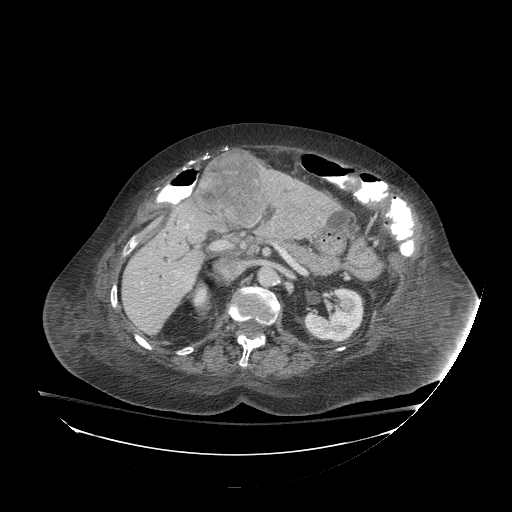
Contrast-enhanced abdominal CT (liver protocol), one axial slice; position 40 of 81 along the scan axis; 140 kVp; soft-tissue window (W 400 / L 40 HU); 2.5 mm slice thickness; 512 × 512 image matrix. From the clinical record (not read from this slice): diagnosis: hepatocellular carcinoma (patient treated with transarterial chemoembolisation; whether this scan precedes or follows treatment is not stated here); TNM stage (as recorded): Stage-I; Child-Pugh class: B; tumour nodularity: uninodular.
Outlined on this slice (semi-automatically segmented with operator editing):
- liver parenchyma outside the tumour (the mass and vessels are separate outlines, so this box may not span the whole liver): bounding box (x1, y1, x2, y2) in pixels: (122, 182, 338, 334)
- mass: (197, 151, 267, 226)
- liver vessels: (178, 224, 189, 275)